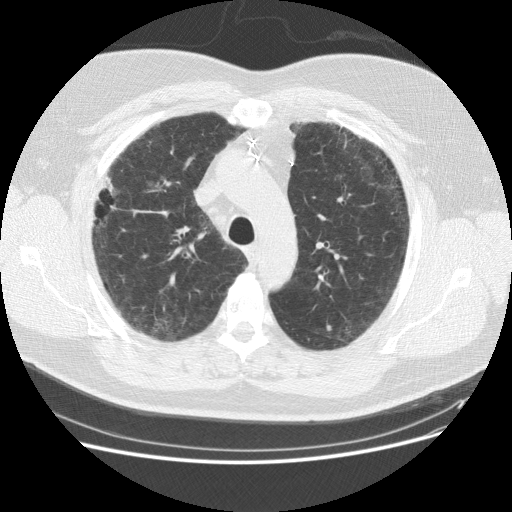
Chest CT (low-dose screening protocol), one axial image, baseline screening round, lung window (W 1500 / L -600 HU), 2.5 mm slice thickness, standard (soft-tissue) reconstruction kernel (STANDARD), 120 kVp. Male participant, aged 59 years at enrolment.
• Lesion marked by an expert reader, box from (x=79, y=161) to (x=138, y=239) px.
• The screening reader recorded 2 non-calcified nodules or masses ≥4 mm on this exam (right middle lobe, right lower lobe); which of them this box marks is not recorded.
• Participant outcome: lung cancer diagnosed 338 days after this screen — adenocarcinoma, NOS, right upper lobe, right middle lobe, moderately differentiated (G2), stage IA (AJCC 6th edition), 13 mm at pathology.